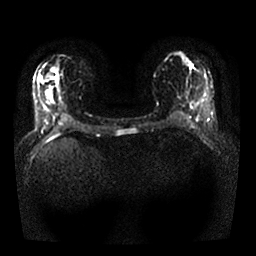
Breast MRI, one axial slice; slice 13 of 25 in the series (ordered by position); diffusion-weighted series; image 2 of 4 stored at this slice position (different b-values; order by instance number); 1.5 T; 4 mm slice thickness; 256 × 256 image matrix. Female patient.
Structures marked on this image (manually delineated by an expert):
- tumour on diffusion-weighted imaging: bounding box (x1, y1, x2, y2) in pixels: (54, 76, 58, 79)